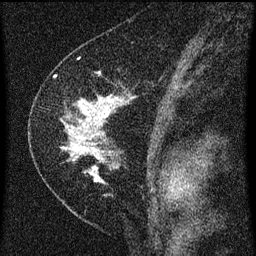
Breast MRI (dynamic contrast-enhanced), one sagittal slice. Position 39 of 60 along the scan axis. Dynamic contrast-enhanced series, image 2 of 3 at this slice position (ordered by acquisition). 1.5 T. TE 4.2 ms, TR 8 ms. 2 mm slice thickness. 256 × 256 image matrix, field of view 180 × 180 mm. Female patient, age 47 years.
Structures marked on this image (semi-automatically segmented with operator editing):
- analysis volume of interest (the breast-tissue region the enhancement analysis was run in; not a lesion): box from (x=38, y=84) to (x=133, y=189) px
- tumour enhancement mask (voxels above the 70 % enhancement threshold inside the analysis volume of interest): (x=65, y=98)–(x=119, y=183)